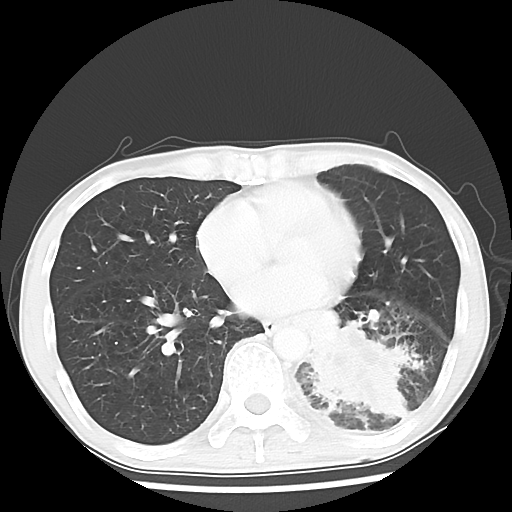
Chest CT, one axial slice. Slice 24 of 64 in the series (ordered by position). Reconstruction kernel LUNG. Lung window (W 1500 / L -600 HU). 5 mm slice thickness. 512 × 512 image matrix, field of view 313 × 313 mm. Patient: male, 68 years. Case-level facts recorded for this patient, not image findings: clinical TNM (as recorded): T4 N0 M0.
Annotated regions visible in this slice (bounding box drawn by a radiologist):
- lung tumour (recorded histology: squamous cell carcinoma): bounding box [x1, y1, x2, y2] px = [298, 318, 421, 430]